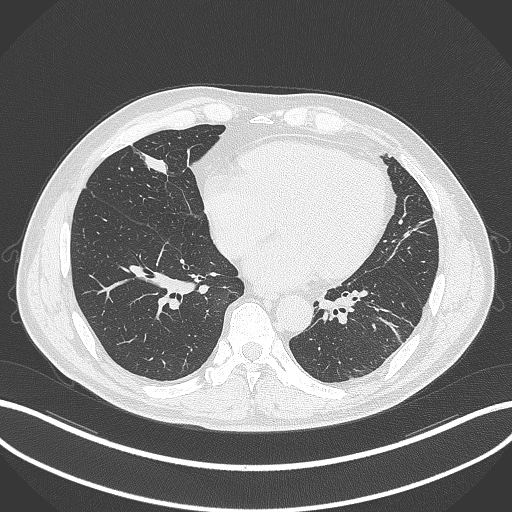
Chest CT, one axial slice; slice 96 of 399 in the series (ordered by position); reconstruction kernel B70f; lung window (W 1500 / L -600 HU); 512 × 512 image matrix. Male patient, age 59 years. From the clinical record (not read from this slice): clinical TNM (as recorded): T2a N1 M0.
Outlined on this slice (rectangle marked by the reading radiologist):
- lung tumour (recorded histology: adenocarcinoma): bounding box (x1, y1, x2, y2) in pixels: (137, 143, 180, 182)